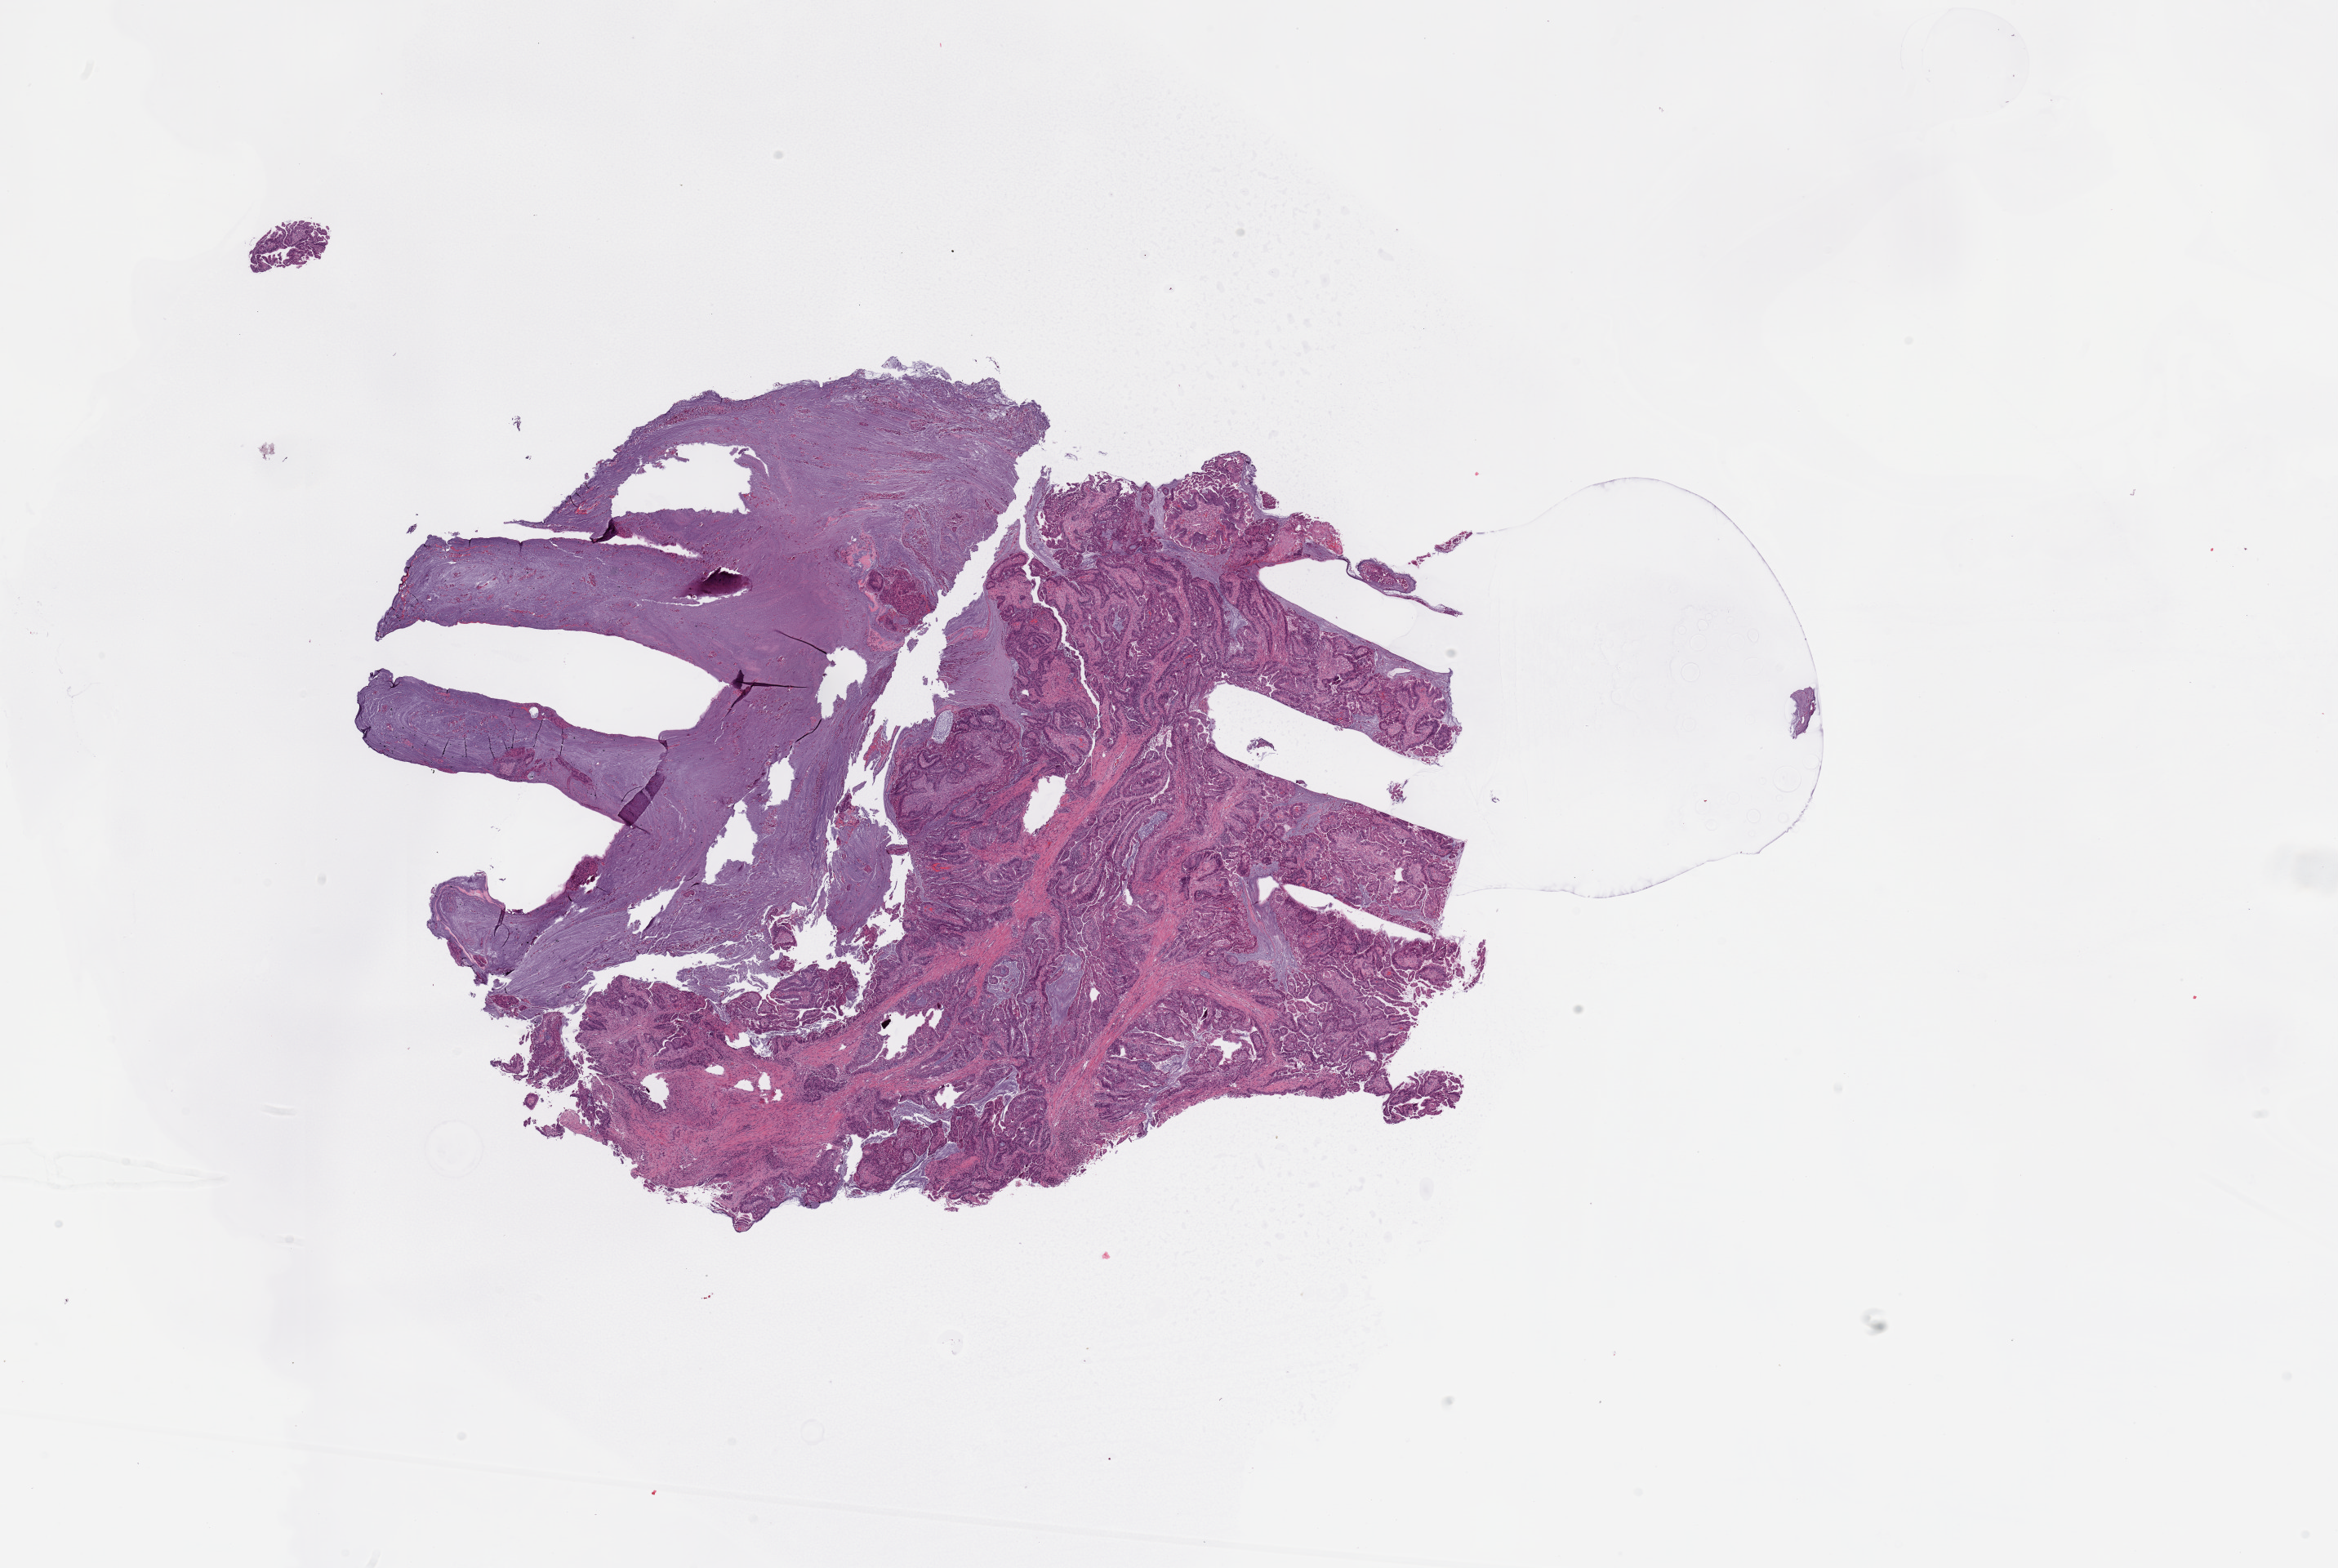
Digitized Hematoxylin and eosin (H&E) stained tissue section (whole slide) — shown as a low-resolution overview of the whole scanned area (about 22.6 x 15.2 mm, acquisition: 20x scan). Tumour tissue sample, uterus. Patient: female, age 46 years. Histologic grade: G2 (moderately differentiated).
AJCC pathologic stage: I. Diagnosis: Endometrioid adenocarcinoma, NOS.